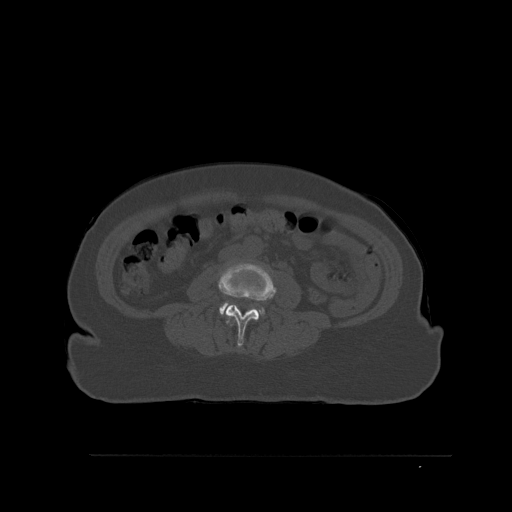
CT including the spine, one axial slice. Position 221 of 527 along the scan axis. Bone window (W 1800 / L 400 HU). 1.5 mm slice thickness. 512 × 512 image matrix, field of view 470 × 470 mm. Female patient, age 73 years. From the clinical record (not read from this slice): primary cancer: breast.
Annotated regions visible in this slice (semi-automatic segmentation, software-assisted and operator-edited):
- L2 vertebra: bounding box [x1, y1, x2, y2] px = [229, 320, 235, 326]
- L3 vertebra: [217, 260, 277, 347]
- L4 vertebra: [219, 301, 265, 315]